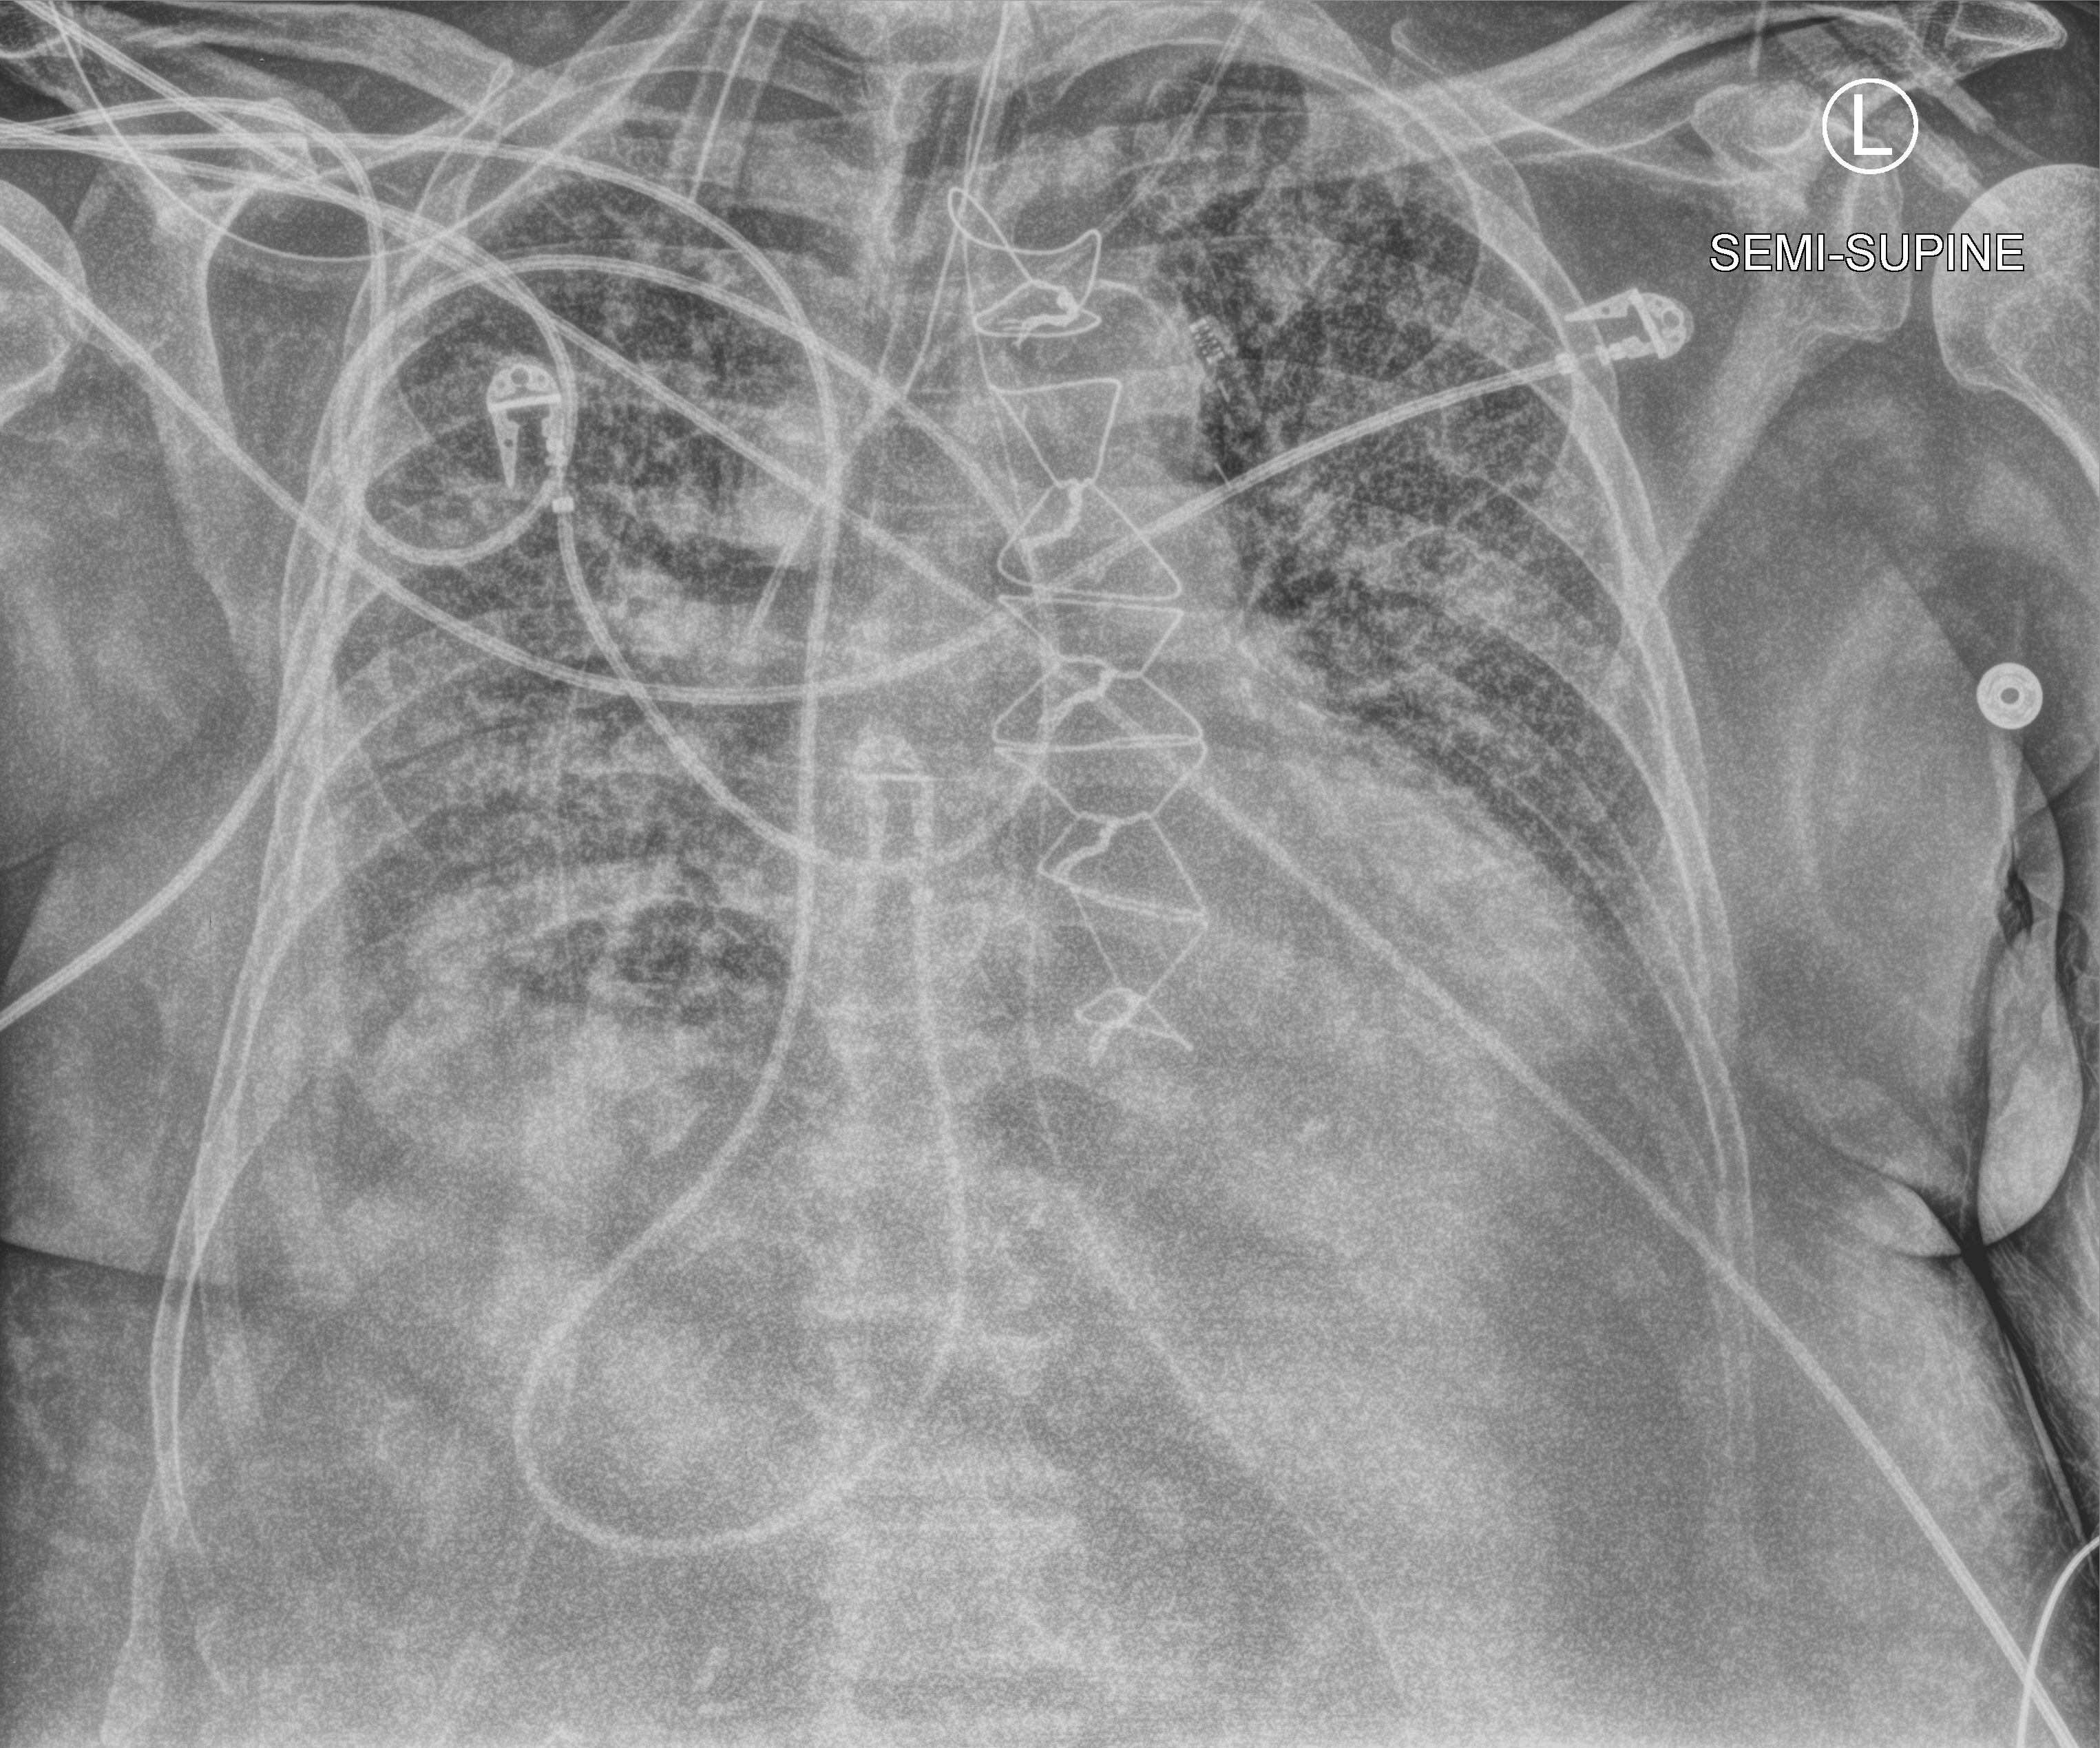
Portable chest radiograph, anteroposterior (AP) projection. Male patient hospitalised with COVID-19, age 75–90 years.
Admission-level facts for this patient (not findings on this image; timing relative to this image not recorded): mechanically ventilated during this hospital stay: yes.